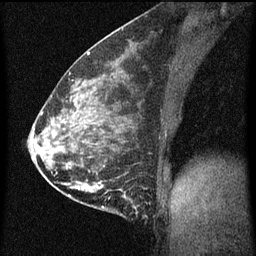
Breast MRI (dynamic contrast-enhanced), one sagittal slice. Position 28 of 60 along the scan axis. Dynamic contrast-enhanced series, image 2 of 3 at this slice position (ordered by acquisition). 1.5 T. TE 4.2 ms, TR 8 ms. 2 mm slice thickness. 256 × 256 image matrix, field of view 180 × 180 mm. Female patient, age 35 years.
Structures marked on this image (semi-automatically segmented with operator editing):
- analysis volume of interest (the breast-tissue region the enhancement analysis was run in; not a lesion): bounding box [x1, y1, x2, y2] px = [110, 180, 156, 219]
- tumour enhancement mask (voxels above the 70 % enhancement threshold inside the analysis volume of interest): [121, 190, 137, 209]